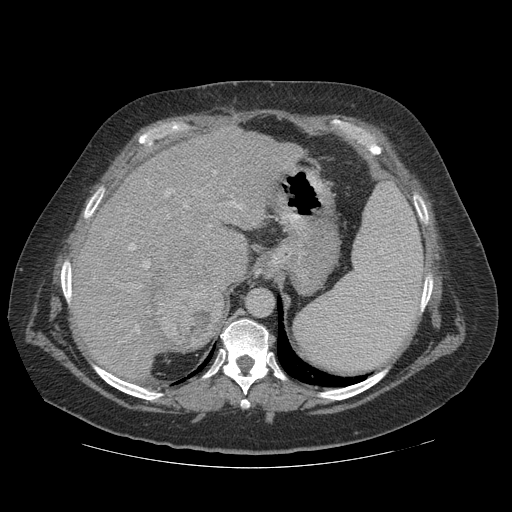
Contrast-enhanced abdominal CT (liver protocol), one axial slice. Position 86 of 121 along the scan axis. 140 kVp. Soft-tissue window (W 400 / L 40 HU). 512 × 512 image matrix, field of view 420 × 420 mm. Case-level facts recorded for this patient, not image findings: diagnosis: hepatocellular carcinoma (patient treated with transarterial chemoembolisation; whether this scan precedes or follows treatment is not stated here); TNM stage (as recorded): Stage-IIIA; Child-Pugh class: A; tumour differentiation: well differentiated; tumour nodularity: multinodular.
Outlined on this slice (semi-automatic segmentation, software-assisted and operator-edited):
- liver parenchyma outside the tumour (the mass and vessels are separate outlines, so this box may not span the whole liver): bounding box <72,126,304,378> (left, top, right, bottom; pixels)
- mass: <131,260,224,353>
- liver vessels: <102,170,255,336>